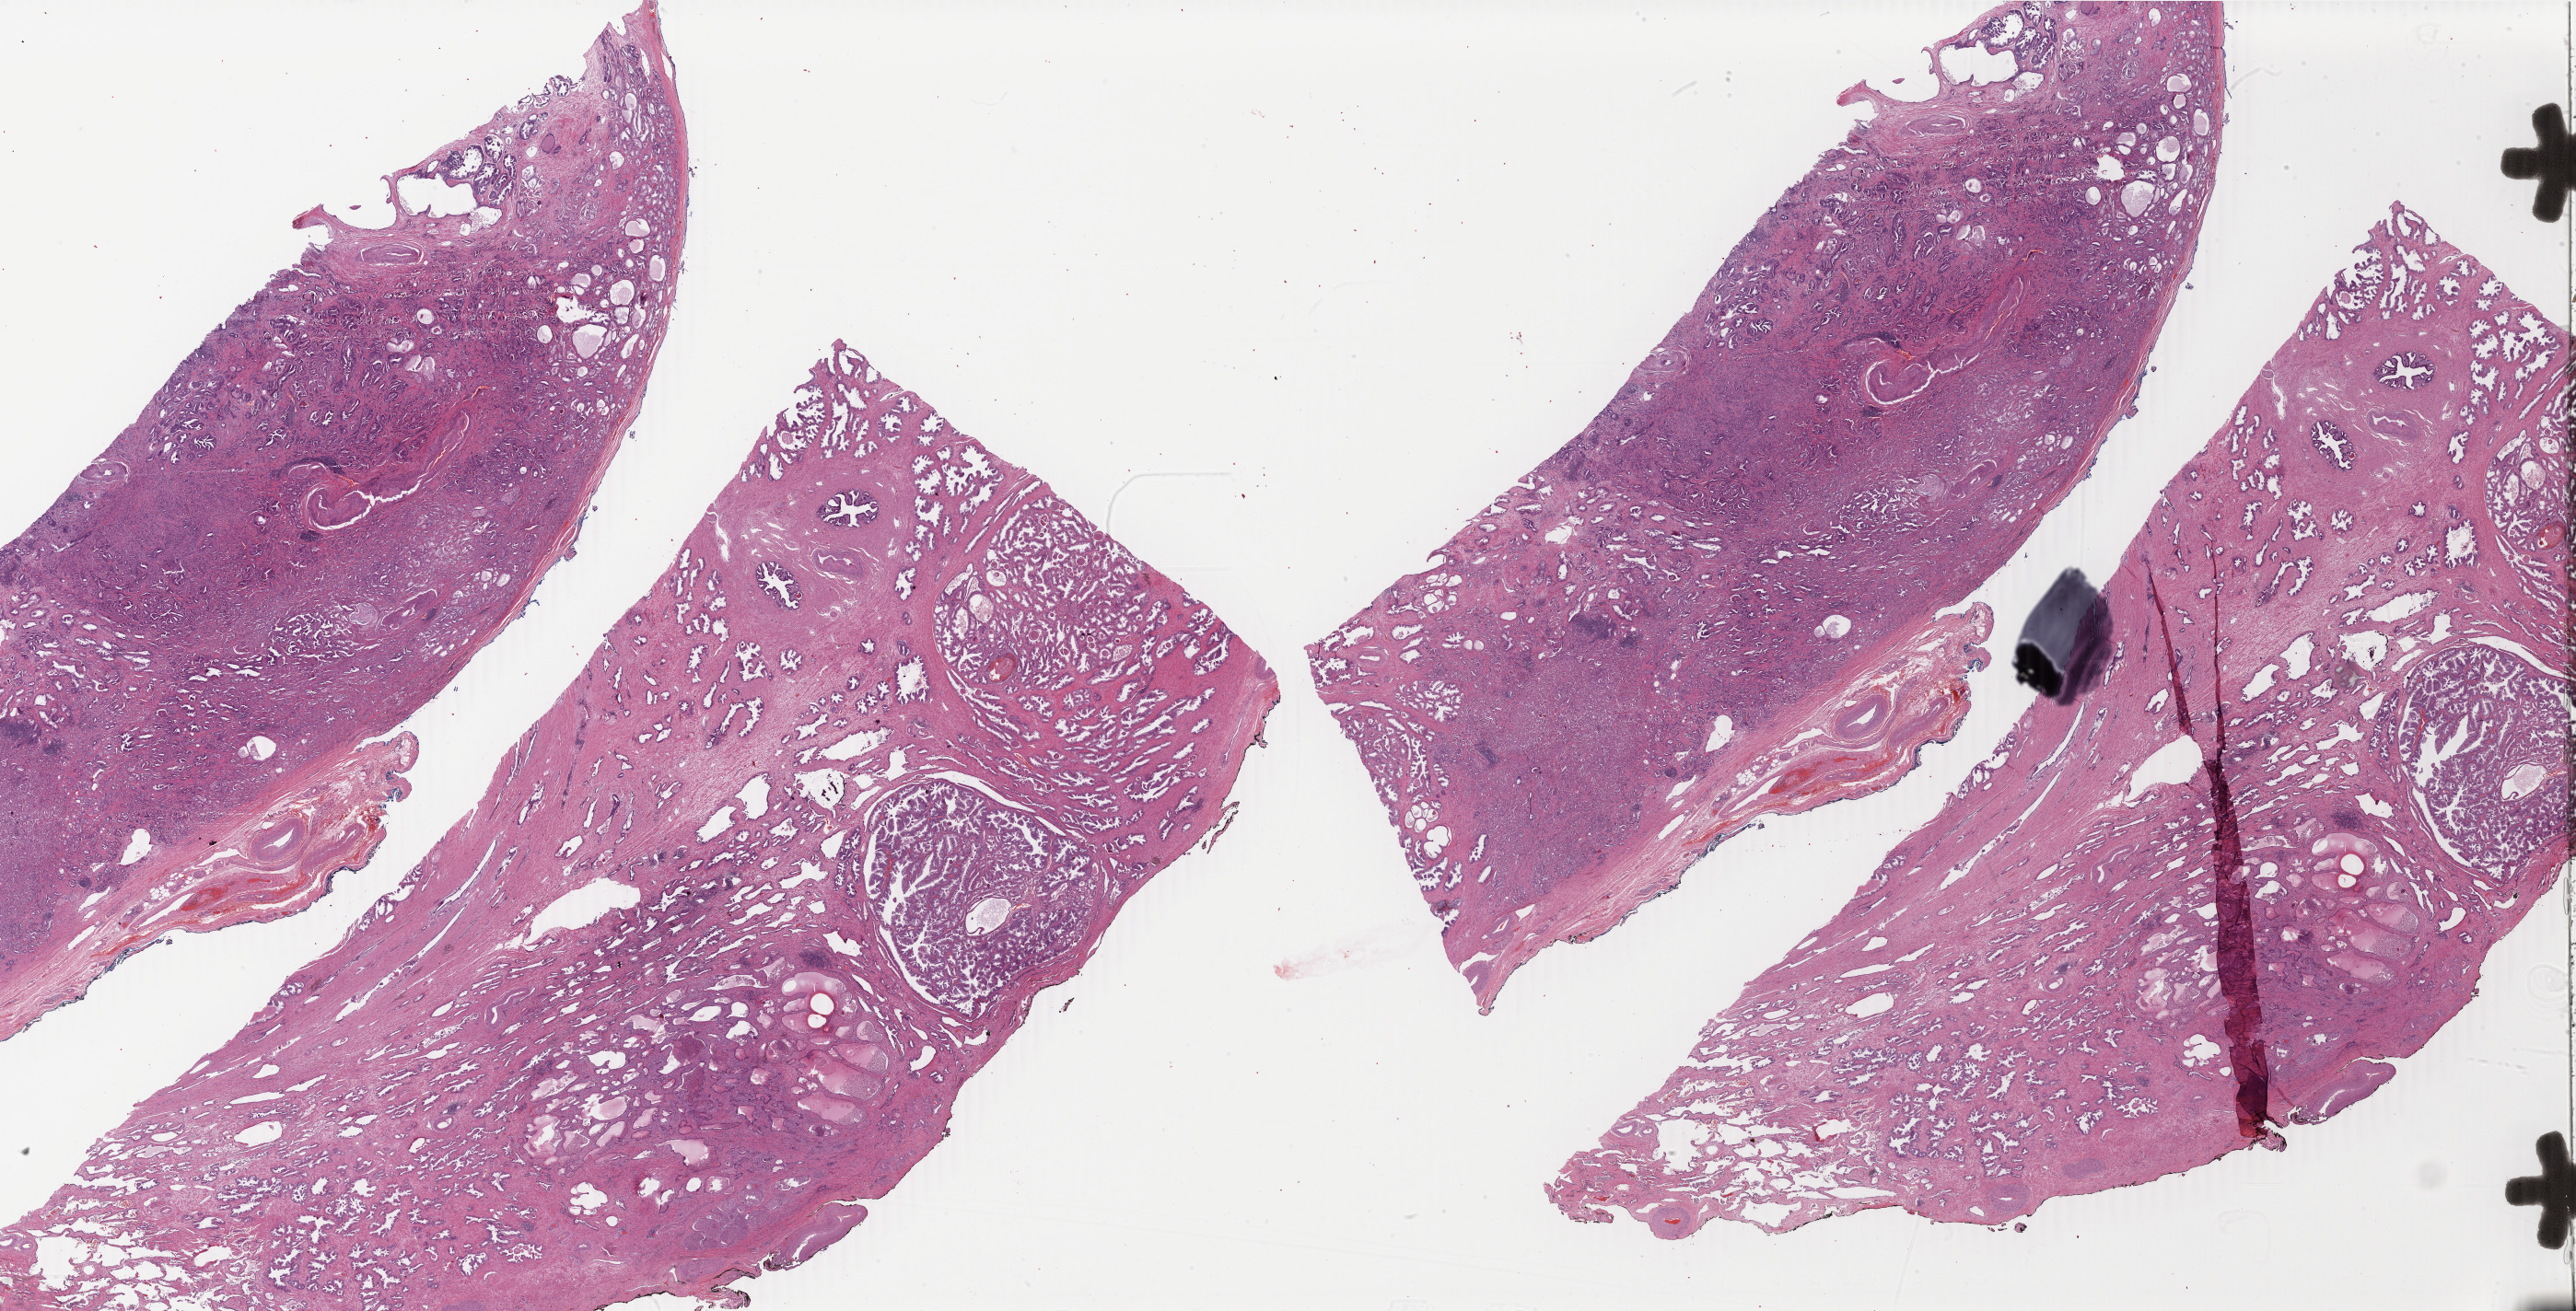
Digitized Hematoxylin and eosin (H&E) stained tissue section (whole slide), whole scanned area (about 44.5 x 22.7 mm) shown as a low-resolution overview; formalin-fixed paraffin-embedded (FFPE) diagnostic section; prostate, primary tumour sample. Male, age 65 years at initial diagnosis. Gleason score: 7 (4+3).
Lymph nodes positive (case pathology): 0 of 4 examined. Histologic diagnosis: Adenocarcinoma, NOS (prostate gland).